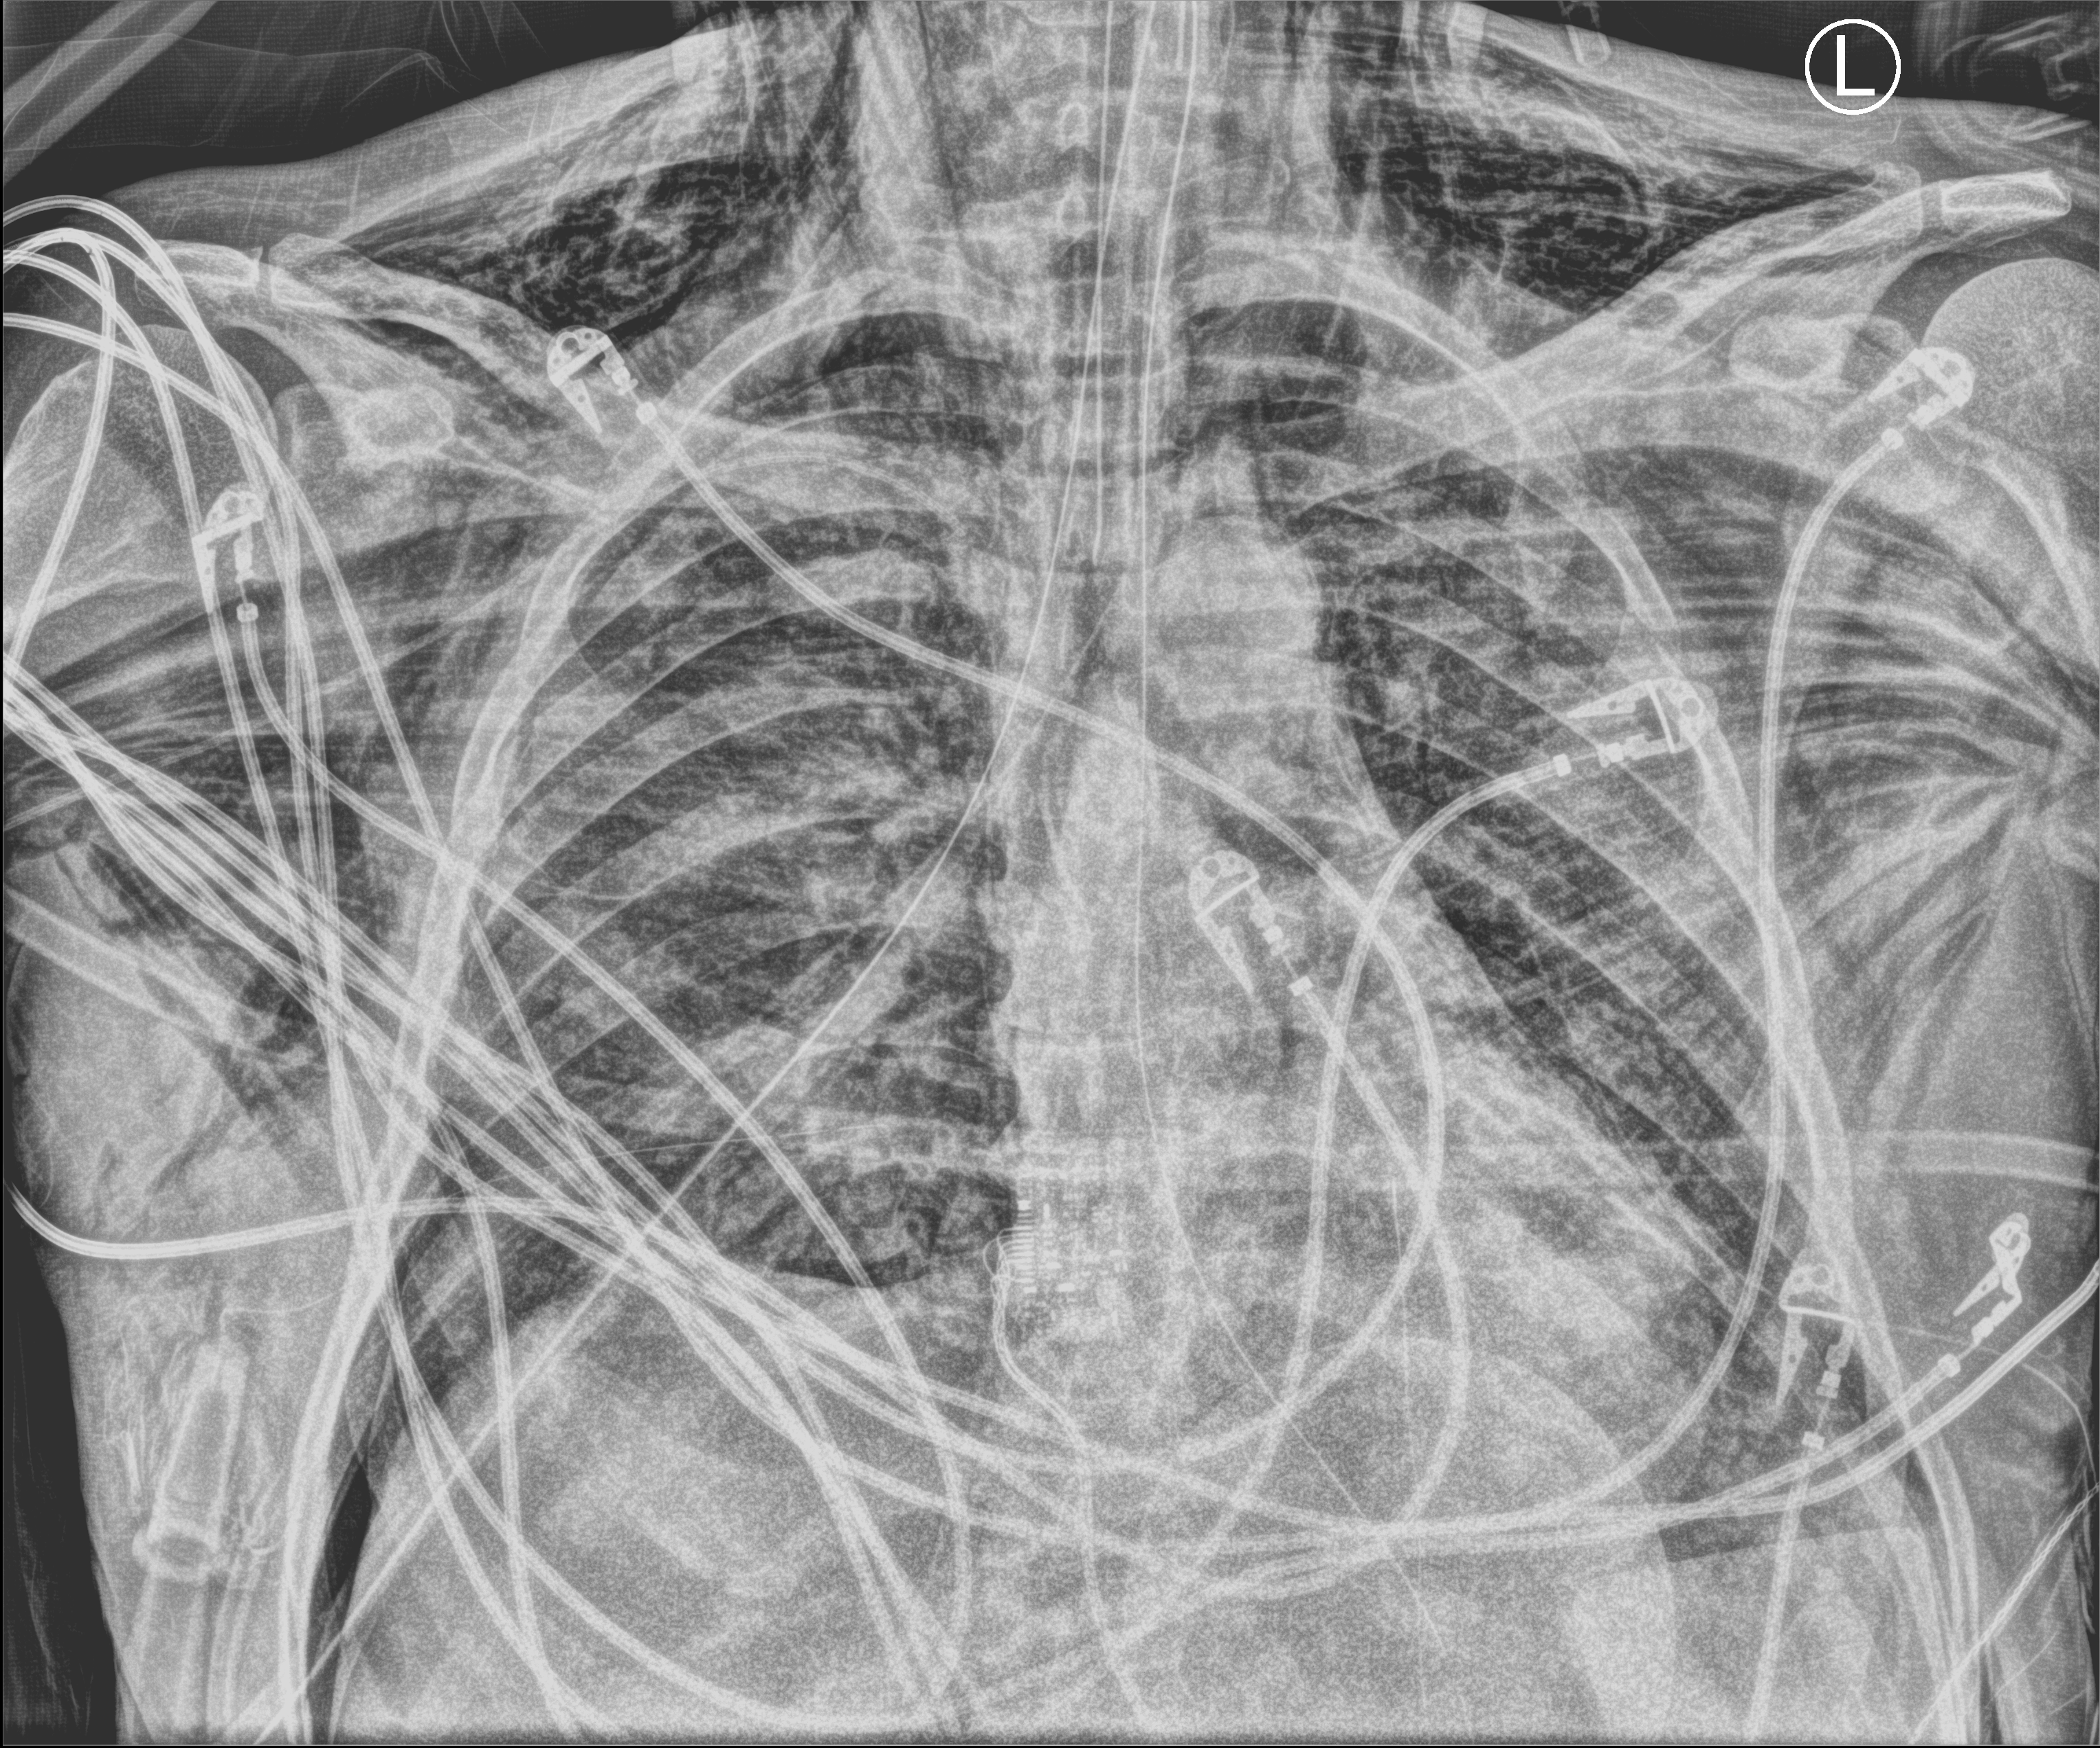
Chest X-ray (portable), anteroposterior (AP) projection. Male patient hospitalised with COVID-19, age 18–59 years.
Admission-level facts for this patient (not findings on this image; timing relative to this image not recorded):
- hypertension (admission record): yes